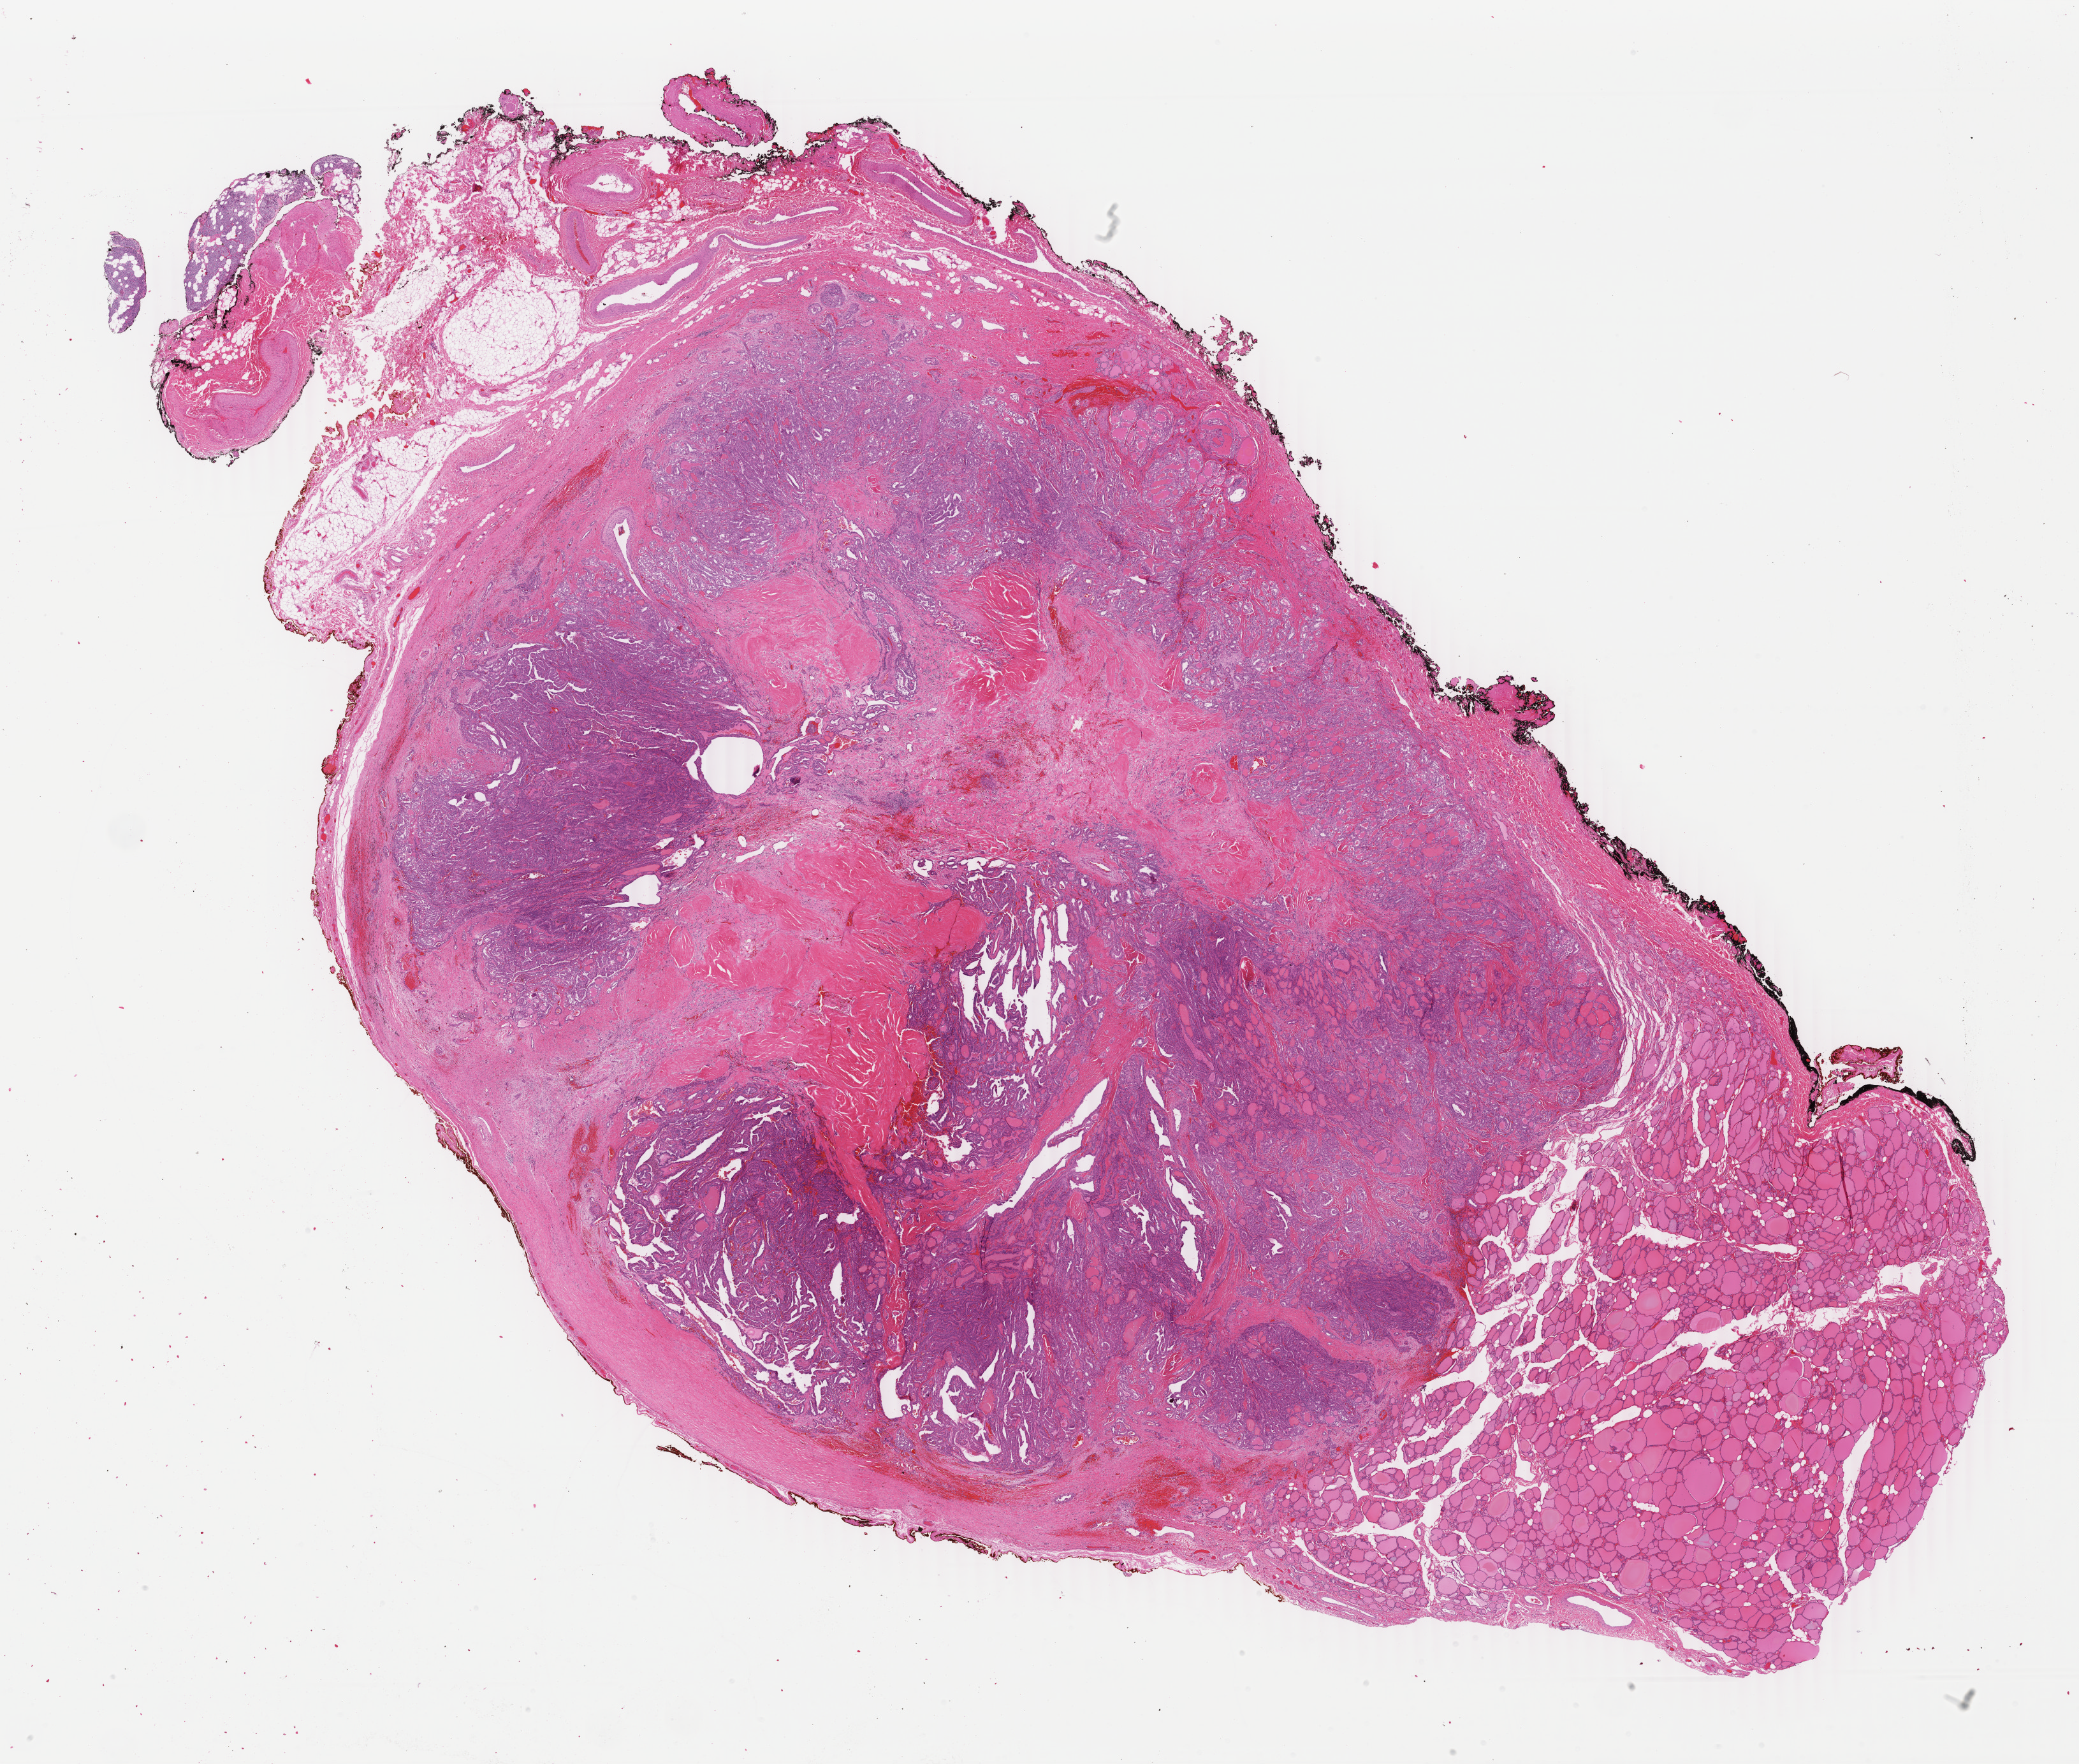
Whole-slide histology image, Hematoxylin and eosin (H&E) stained, a low-resolution overview of the entire scanned area, about 25.9 x 22.0 mm (acquisition: 40x scan). Formalin-fixed paraffin-embedded (FFPE) diagnostic section. Primary tumour sample from the thyroid. Male patient; age at initial diagnosis 33 years.
Histologic diagnosis: Papillary adenocarcinoma, NOS (thyroid gland).